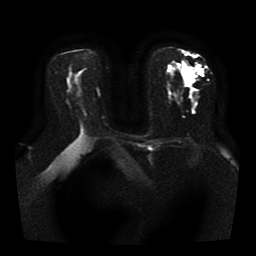
Breast MRI, one axial slice. Position 21 of 41 along the scan axis. Diffusion-weighted series; image 2 of 4 stored at this slice position (different b-values; order by instance number). 1.5 T. 5 mm slice thickness. 256 × 256 image matrix, field of view 330 × 330 mm. Female patient.
Annotated regions visible in this slice (expert manual segmentation):
- tumour on diffusion-weighted imaging: bounding box (x1, y1, x2, y2) in pixels: (187, 66, 203, 82)